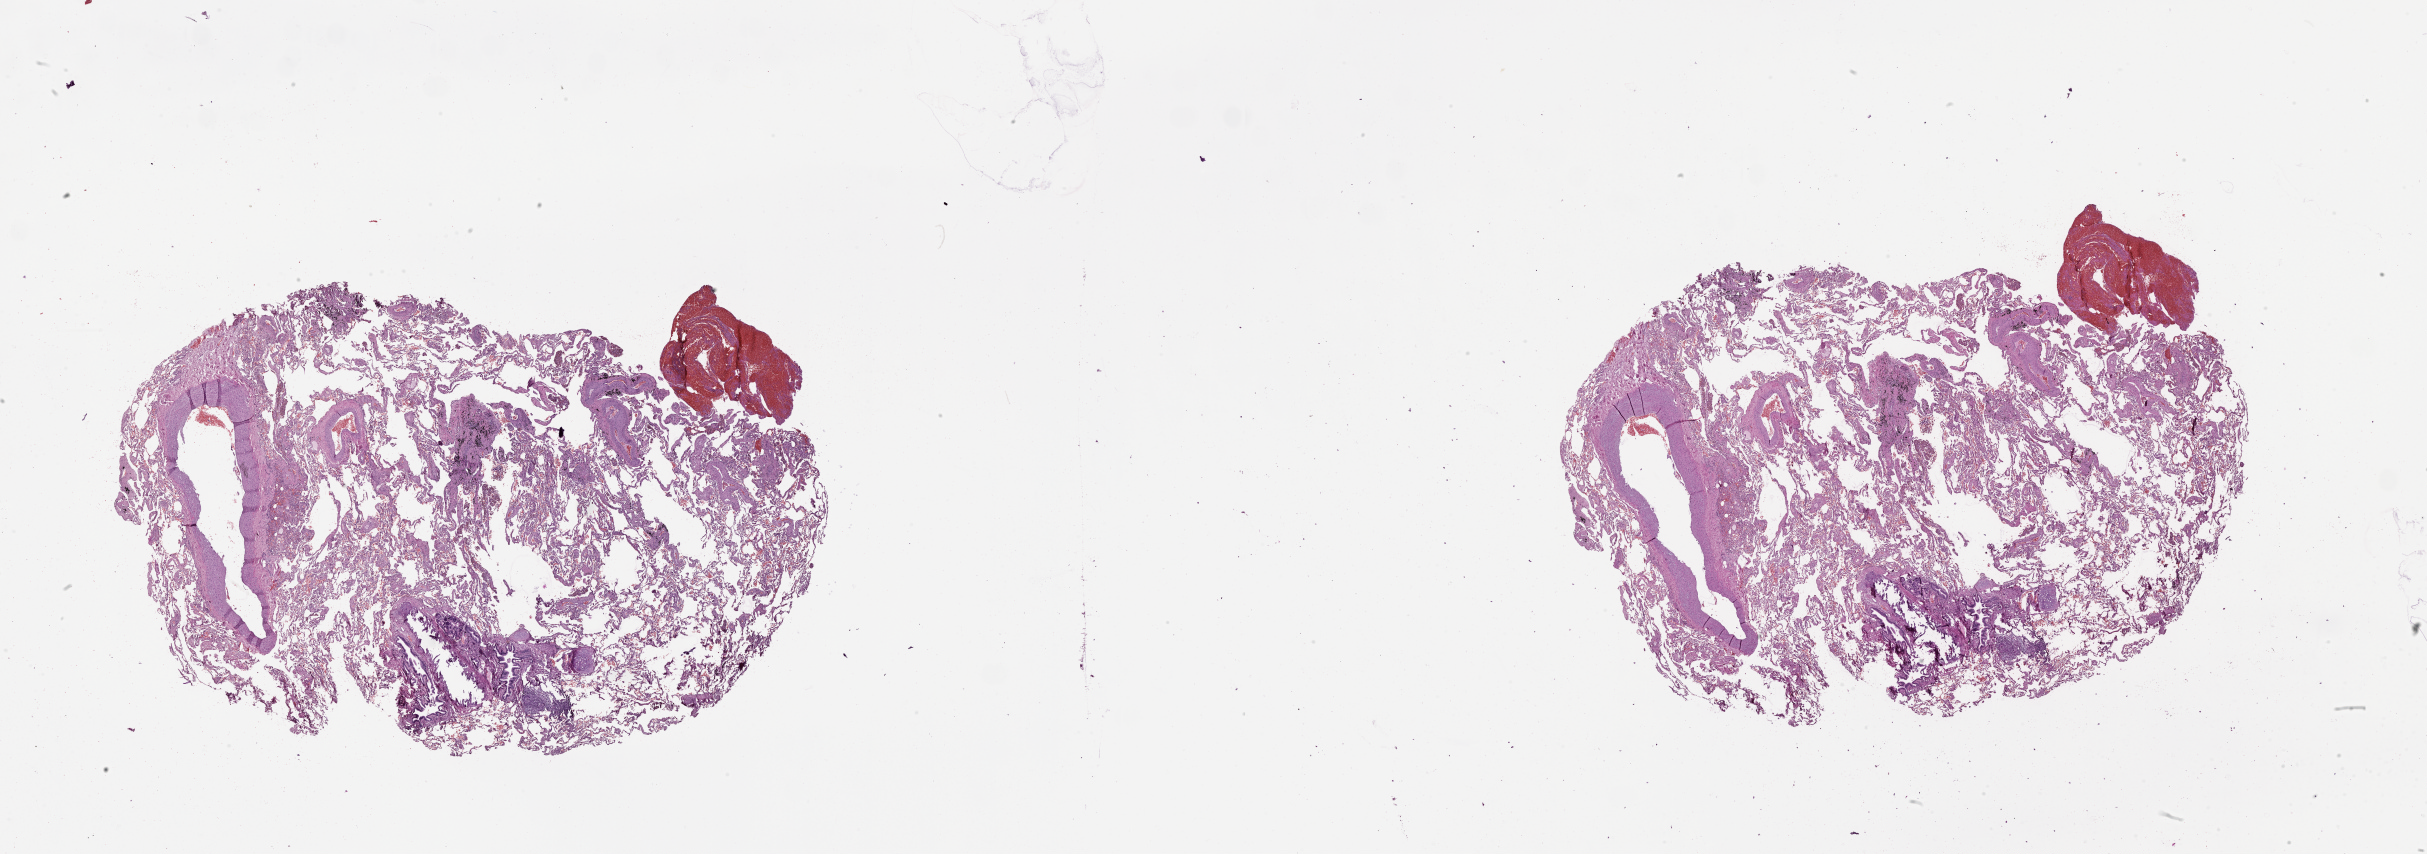
Whole-slide histology image, H&E-stained — whole scanned area (about 39.1 x 13.8 mm, from a 20x scan) shown as a low-resolution overview. Lung, normal (non-tumour) tissue. Patient: male, age 67 years.
- this section: normal (non-tumour) tissue from the same patient
- patient diagnosis (cohort enrolment): squamous cell carcinoma (lung)